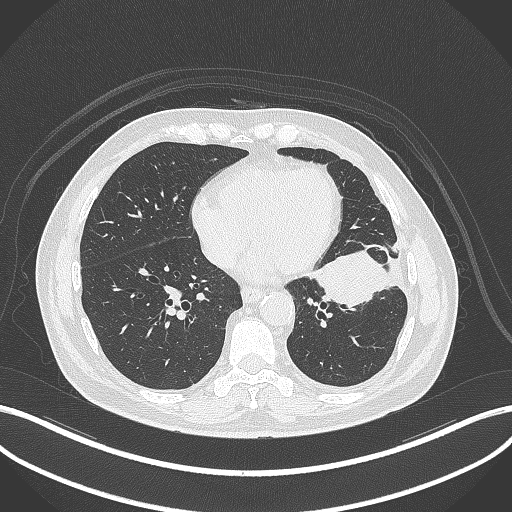
Chest CT, one axial slice; position 131 of 230 along the scan axis; reconstruction kernel B70f; 120 kVp; lung window (W 1500 / L -600 HU); 1 mm slice thickness; 512 × 512 image matrix. Patient: male, 68 years. From the clinical record (not read from this slice): clinical TNM (as recorded): T2b N0 M0.
Outlined on this slice (rectangle marked by the reading radiologist):
- lung tumour (recorded histology: squamous cell carcinoma): bounding box [x1, y1, x2, y2] px = [309, 250, 392, 311]